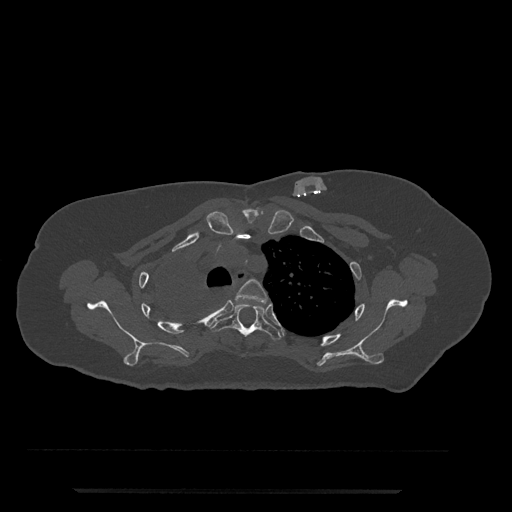
CT including the spine, one axial slice; position 603 of 797 along the scan axis; 120 kVp; bone window (W 1800 / L 400 HU); 0.5 mm slice thickness; 512 × 512 image matrix. Female patient, age 51 years. Case-level facts recorded for this patient, not image findings: primary cancer: neuro; vertebrae with lytic lesions (as recorded): T8.
Annotated regions visible in this slice (semi-automatically segmented with operator editing):
- T3 vertebra: box from (x=235, y=279) to (x=268, y=303) px
- T4 vertebra: (x=210, y=303)–(x=282, y=340)